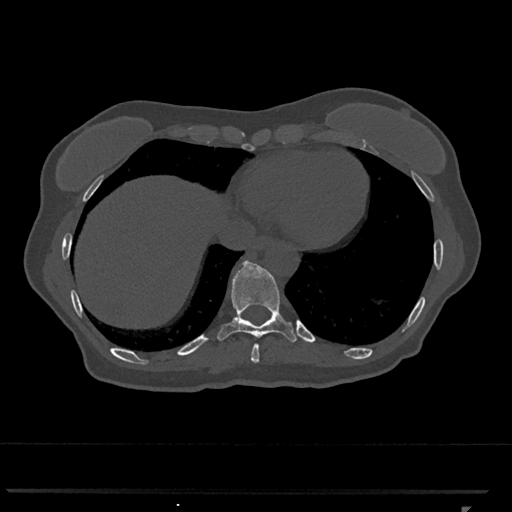
CT including the spine, one axial slice; slice 574 of 793 in the series (ordered by position); 120 kVp; bone window (W 1800 / L 400 HU); 512 × 512 image matrix, field of view 380 × 380 mm. Patient: female, 62 years. From the clinical record (not read from this slice): primary cancer: renal.
Annotated regions visible in this slice (semi-automatic segmentation, software-assisted and operator-edited):
- T10 vertebra: box from (x=217, y=261) to (x=297, y=345) px
- T9 vertebra: (x=251, y=344)–(x=259, y=363)